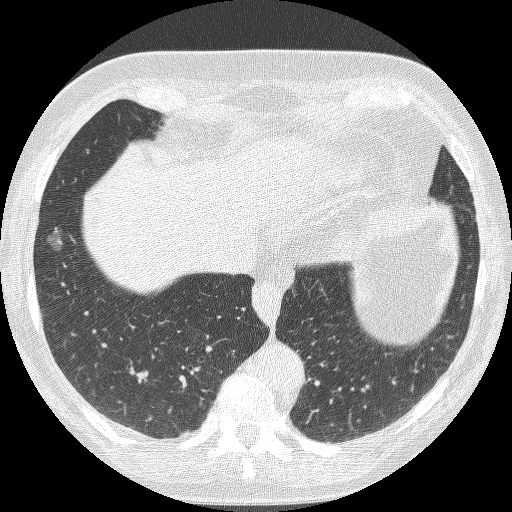
Chest CT (low-dose screening protocol), one axial image. First (baseline) screen. Lung window (W 1500 / L -600 HU). 1.25 mm slice thickness. Lung (sharp) reconstruction kernel (BONE). Slice 65 of 221 in the series. Female, age 68 years at enrolment. Current smoker at enrolment.
Expert-annotated lung lesion, bounding box <35,216,87,264> (left, top, right, bottom; pixels). Reader record for this screening exam (exam-level; its link to the box is not recorded): non-calcified nodule or mass ≥4 mm, right lower lobe, 16 × 12 mm, poorly defined margins, ground glass attenuation. Participant outcome: lung cancer diagnosed 406 days after this screen (after the second annual screen) — bronchiolo-alveolar adenocarcinoma, NOS, right lower lobe, well differentiated (G1), stage IA (AJCC 6th edition), 13 mm at pathology.